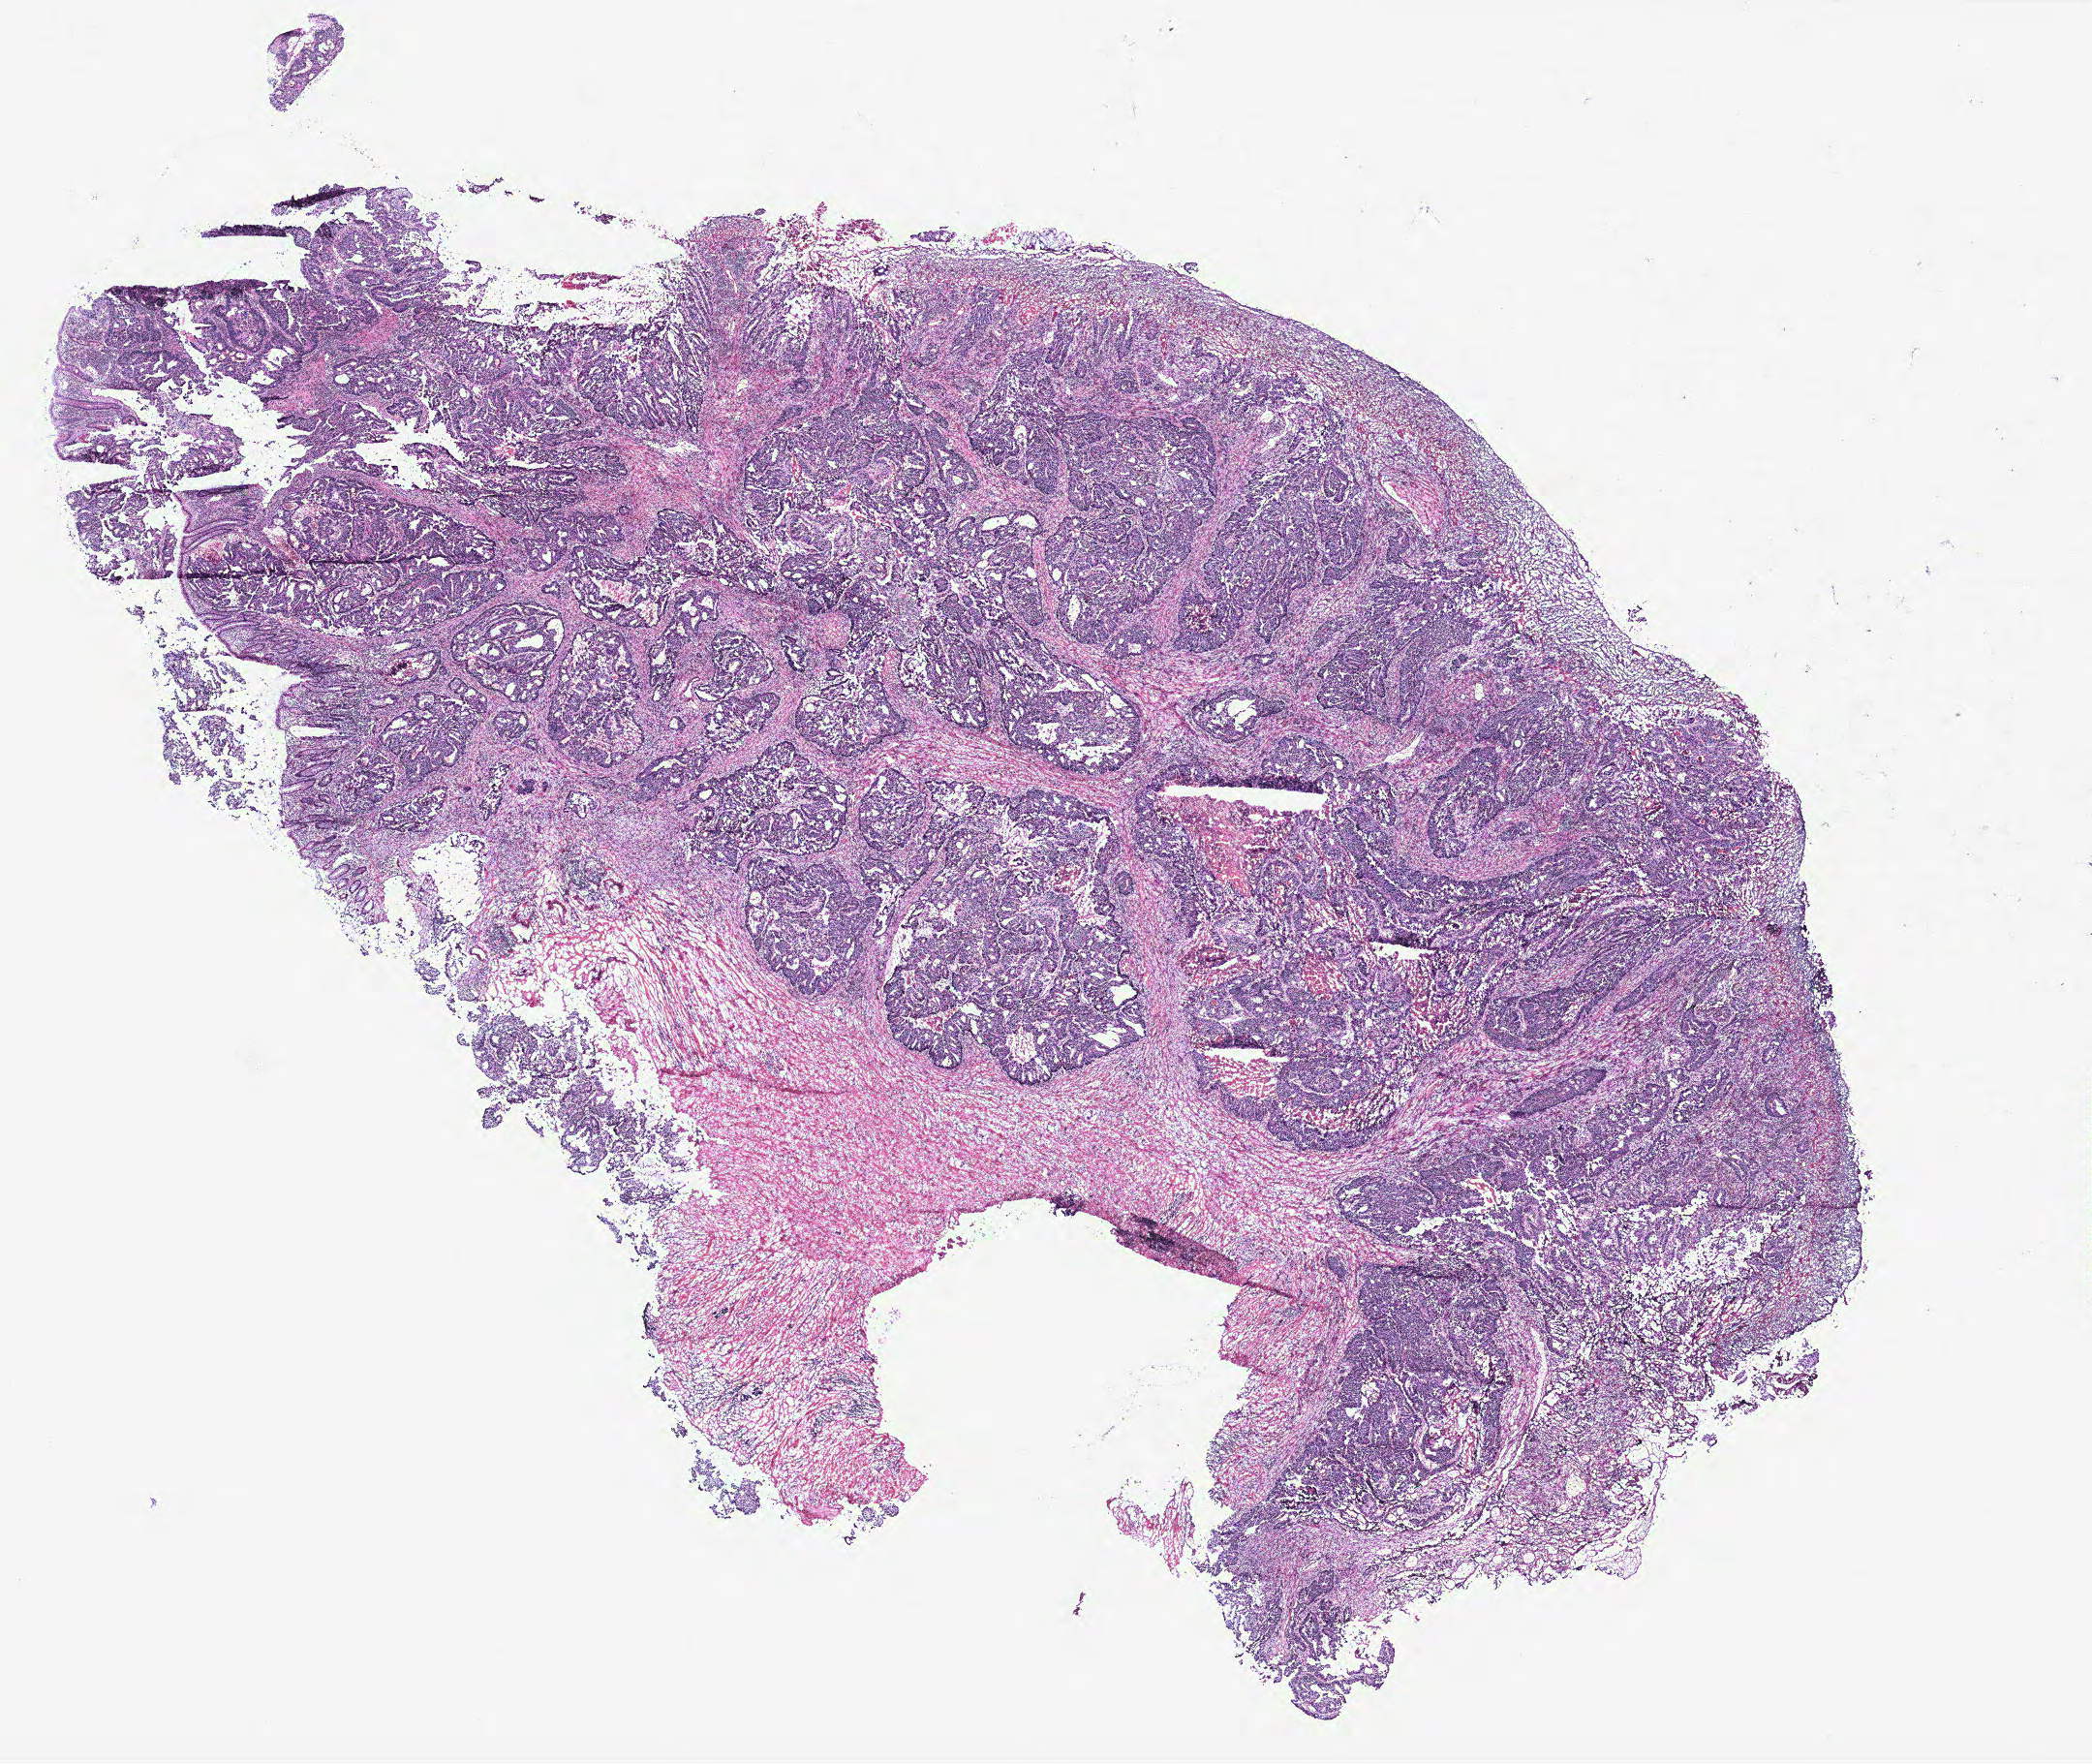
Digitized H&E-stained tissue section (whole slide), shown as a low-resolution overview of the whole scanned area (about 17.3 x 14.6 mm, from a 40x scan). Normal (non-tumour) tissue sample, colon. 72-year-old male patient.
This section: normal (non-tumour) tissue from the same patient. Patient diagnosis: Adenocarcinoma, NOS.